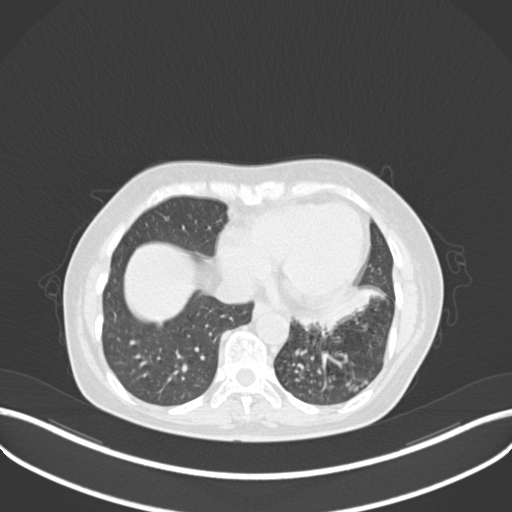
Chest CT, one axial slice; slice 80 of 270 in the series (ordered by position); lung window (W 1500 / L -600 HU); 1 mm slice thickness; 512 × 512 image matrix. Patient: female, 63 years. From the clinical record (not read from this slice): clinical TNM (as recorded): T1b N0 M0; histopathological grade: G2-3.
Outlined on this slice (rectangle marked by the reading radiologist):
- lung tumour (recorded histology: adenocarcinoma): bounding box (x1, y1, x2, y2) in pixels: (295, 284, 388, 336)